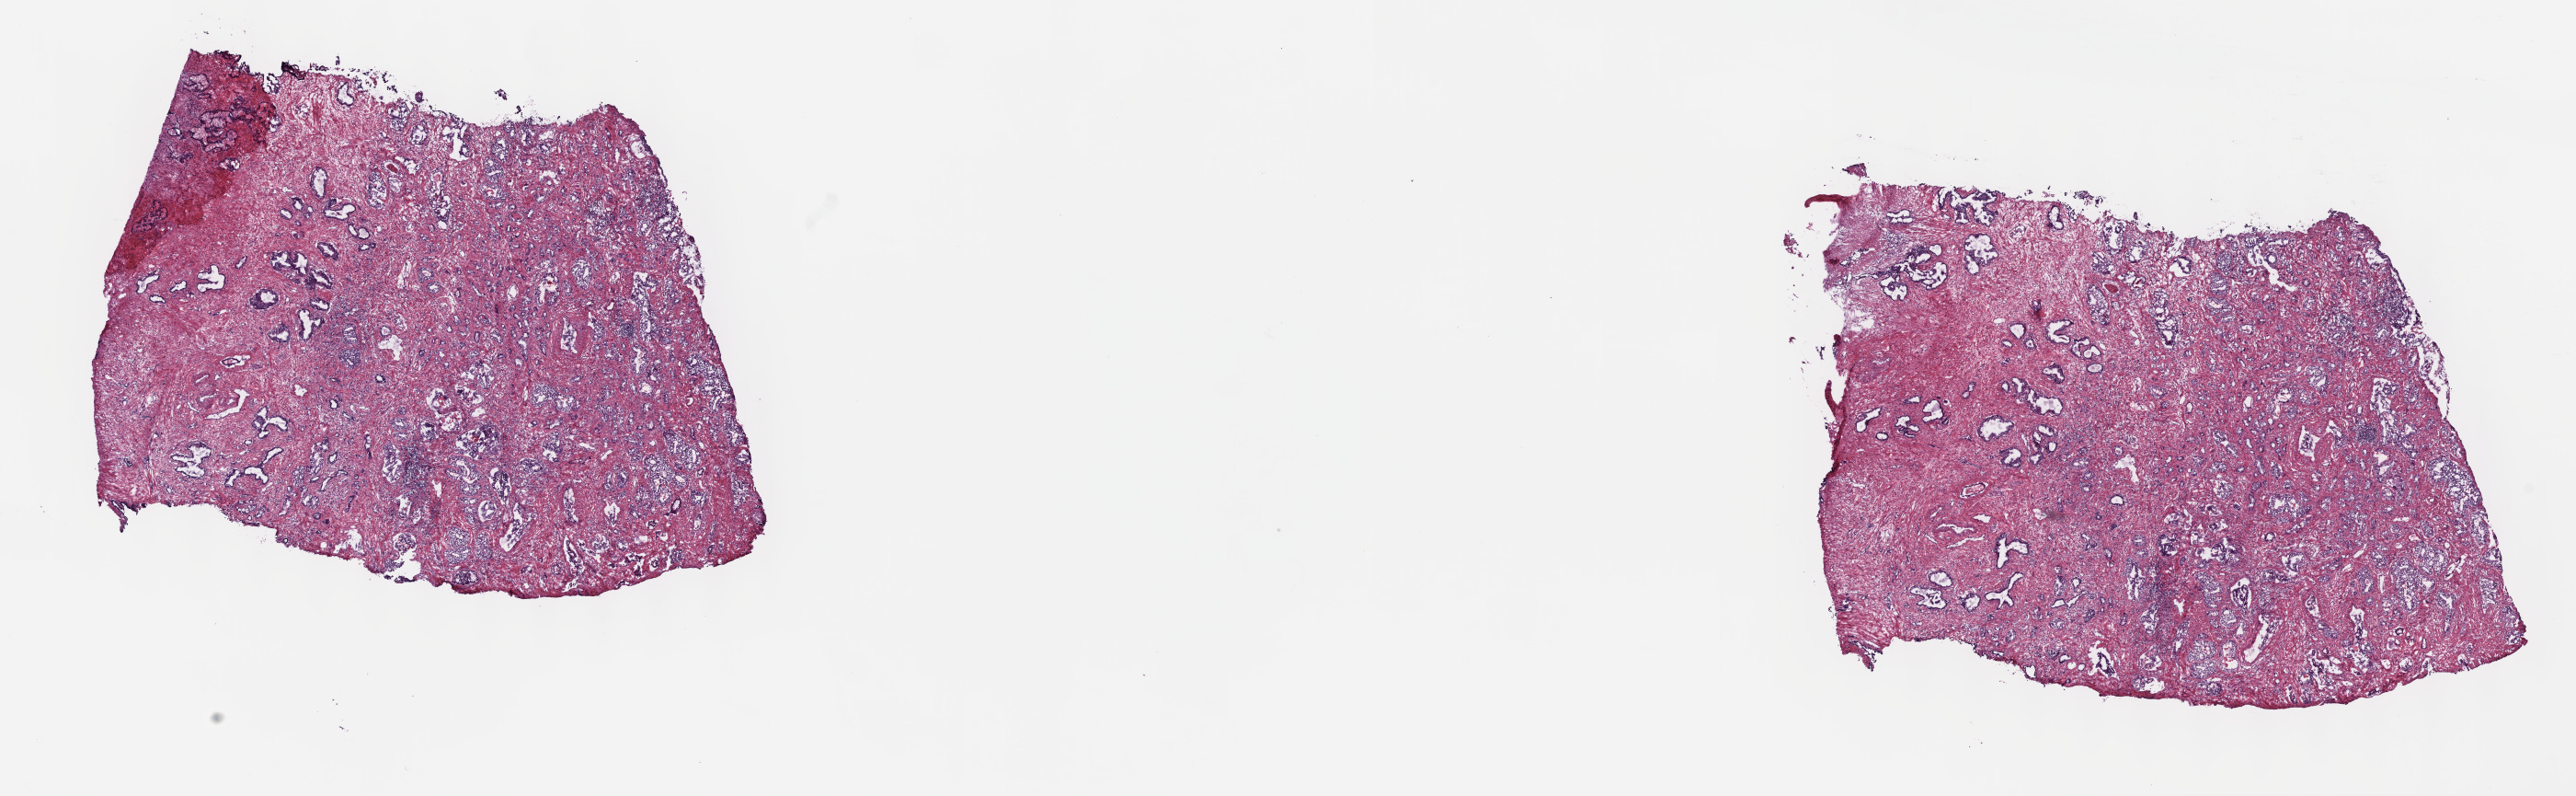
H&E whole-slide image, shown as a low-resolution overview of the whole scanned area (about 22.7 x 7.0 mm, from a 40x scan); frozen section; primary tumour sample from the prostate. Male, age 63 years at initial diagnosis. Slide review estimates, as recorded: tumour cells 50%, tumour nuclei 60%.
Histologic diagnosis: Adenocarcinoma, NOS.